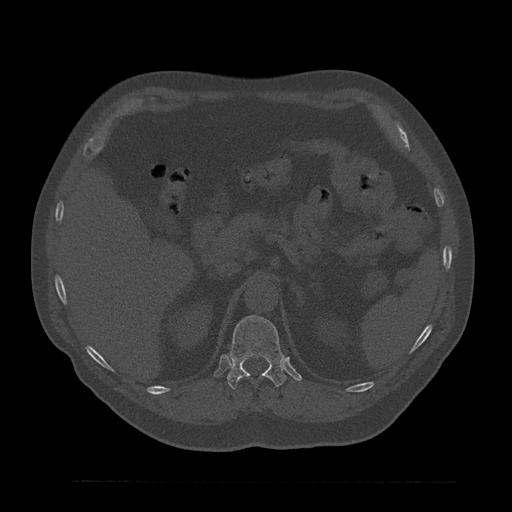
CT including the spine, one axial slice; position 241 of 797 along the scan axis; bone window (W 1800 / L 400 HU); 0.5 mm slice thickness; 512 × 512 image matrix, field of view 430 × 430 mm. Patient: male, 61 years. From the clinical record (not read from this slice): primary cancer: prostate.
Outlined on this slice (semi-automatic segmentation, software-assisted and operator-edited):
- T12 vertebra: bounding box <227,315,287,390> (left, top, right, bottom; pixels)